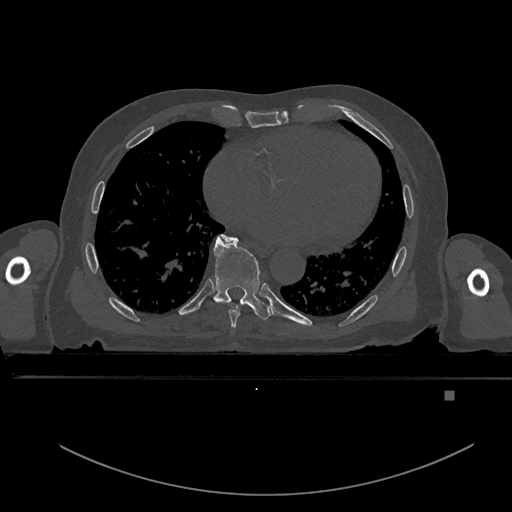
CT including the spine, one axial slice. Bone window (W 1800 / L 400 HU). 0.5 mm slice thickness. 512 × 512 image matrix, field of view 456 × 456 mm. Male patient, age 82 years. From the clinical record (not read from this slice): primary cancer: prostate.
Outlined on this slice (semi-automatically segmented with operator editing):
- T7 vertebra: box from (x=222, y=235) to (x=240, y=327) px
- T8 vertebra: (x=213, y=237)–(x=273, y=320)